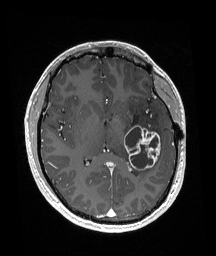
Brain MRI from a brain-tumour surgery series, one axial slice; position 91 of 192 along the scan axis; T1-weighted post-contrast; 216 × 256 image matrix. Case-level facts recorded for this patient, not image findings: histopathology: Glioneuronal tumor; WHO grade: 2; tumour location: Left Superior Temporal Gyrus.
Outlined on this slice (expert manual segmentation):
- tumour: bounding box <124,125,161,171> (left, top, right, bottom; pixels)